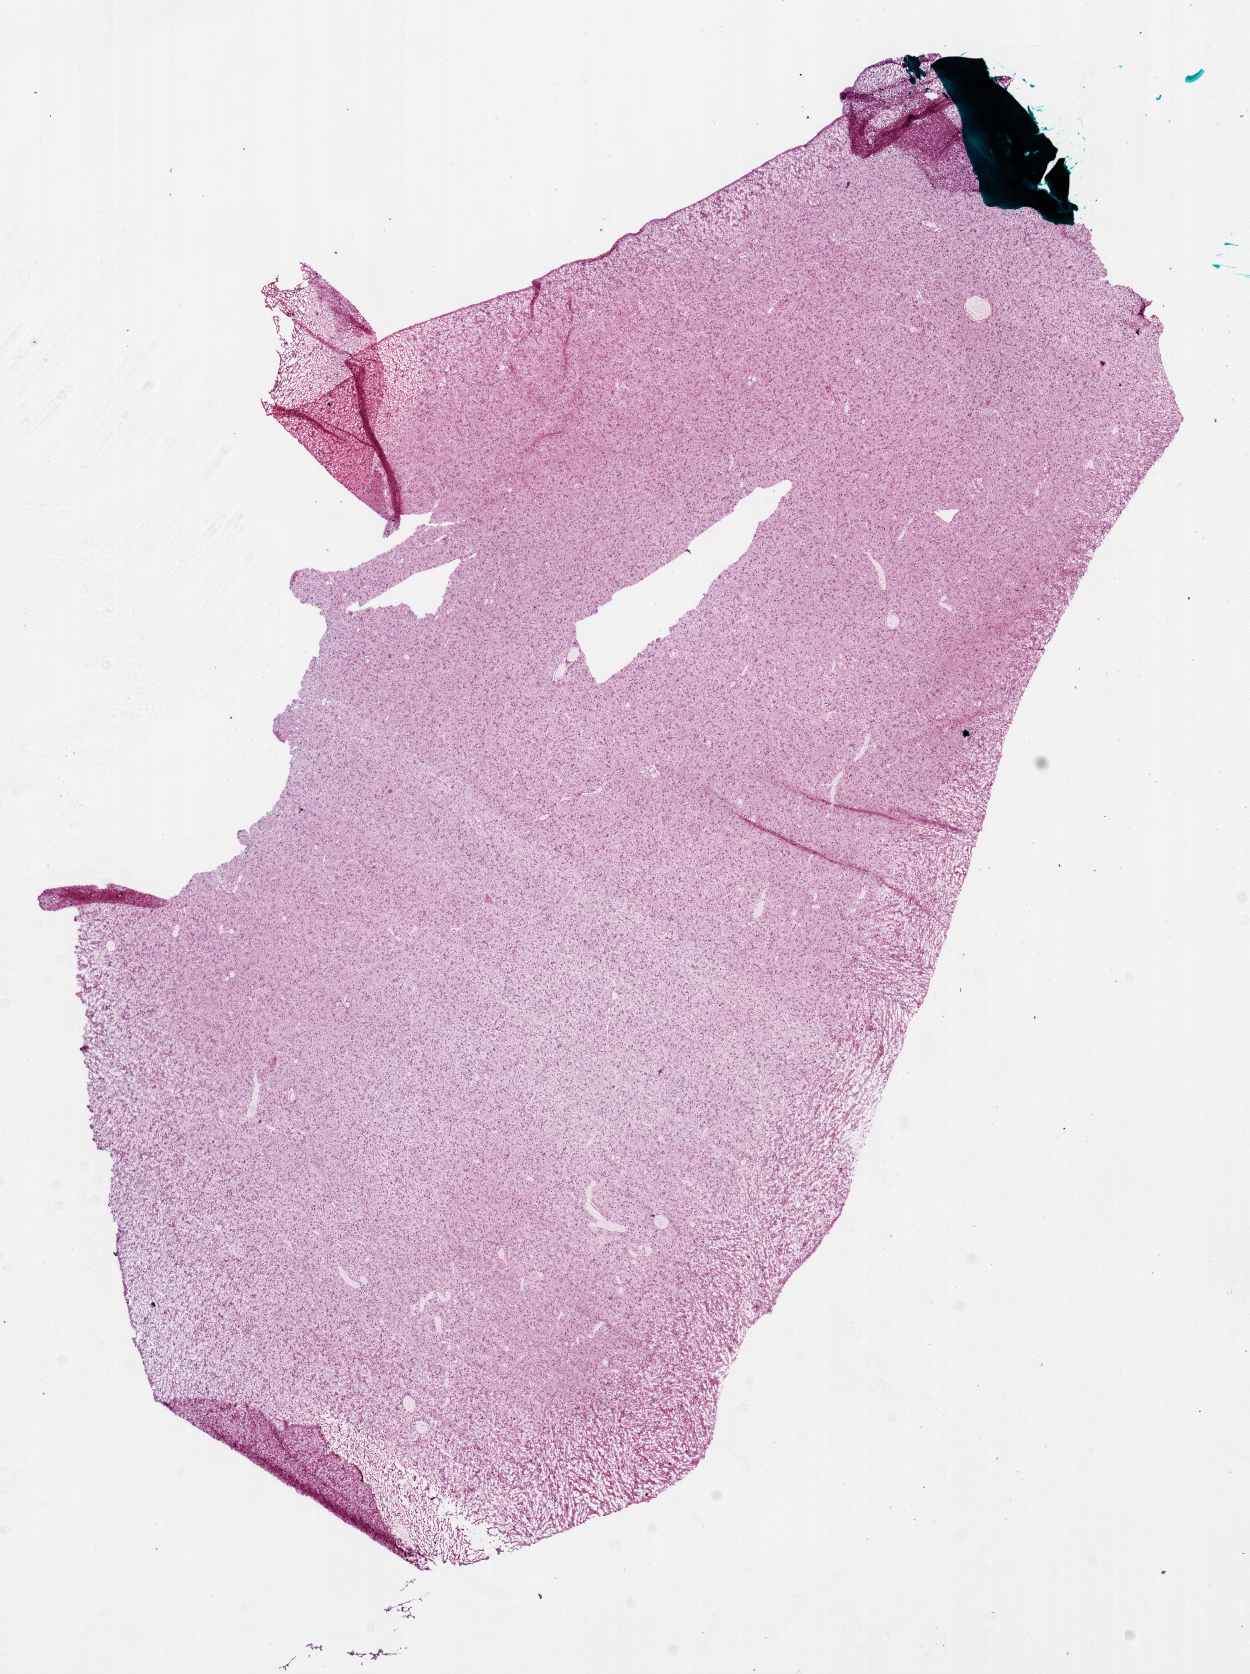
Whole-slide histology image, H&E, whole scanned area (about 10.0 x 13.4 mm, from a 20x scan) shown as a low-resolution overview. Frozen section from the bottom of the tissue portion. Sample: primary tumour, brain. Male, age 60 years at initial diagnosis.
Histologic diagnosis: Glioblastoma.